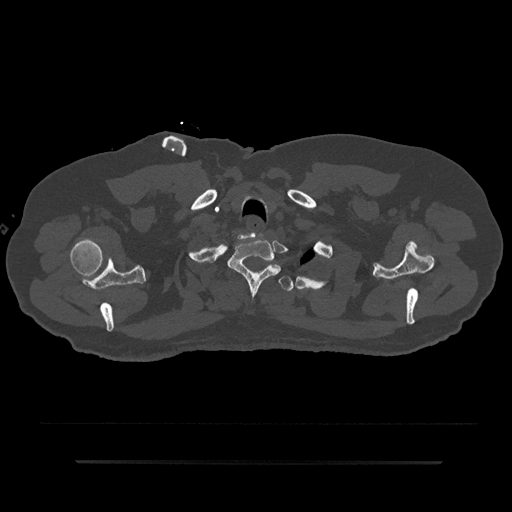
CT including the spine, one axial slice; position 731 of 797 along the scan axis; 120 kVp; bone window (W 1800 / L 400 HU); 0.5 mm slice thickness; 512 × 512 image matrix. Male patient, age 59 years. Case-level facts recorded for this patient, not image findings: primary cancer: bile ducts.
Annotated regions visible in this slice (semi-automatically segmented with operator editing):
- T1 vertebra: bounding box (x1, y1, x2, y2) in pixels: (228, 237, 281, 297)
- T2 vertebra: (221, 264, 293, 291)